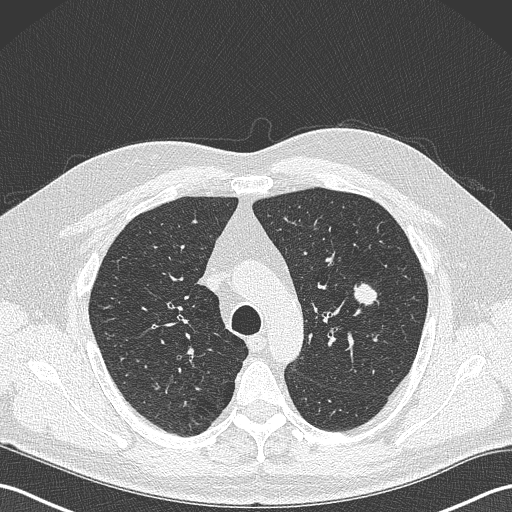
Low-dose screening chest CT, one axial slice. Slice 249 of 343 in the series (ordered by position). Lung window (W 1500 / L -600 HU). 1 mm slice thickness. 512 × 512 image matrix, field of view 350 × 350 mm.
Outlined on this slice (outlined manually by an expert reader):
- lesion 1 (tumor, upper lobe of left lung): bounding box <354,282,381,306> (left, top, right, bottom; pixels)